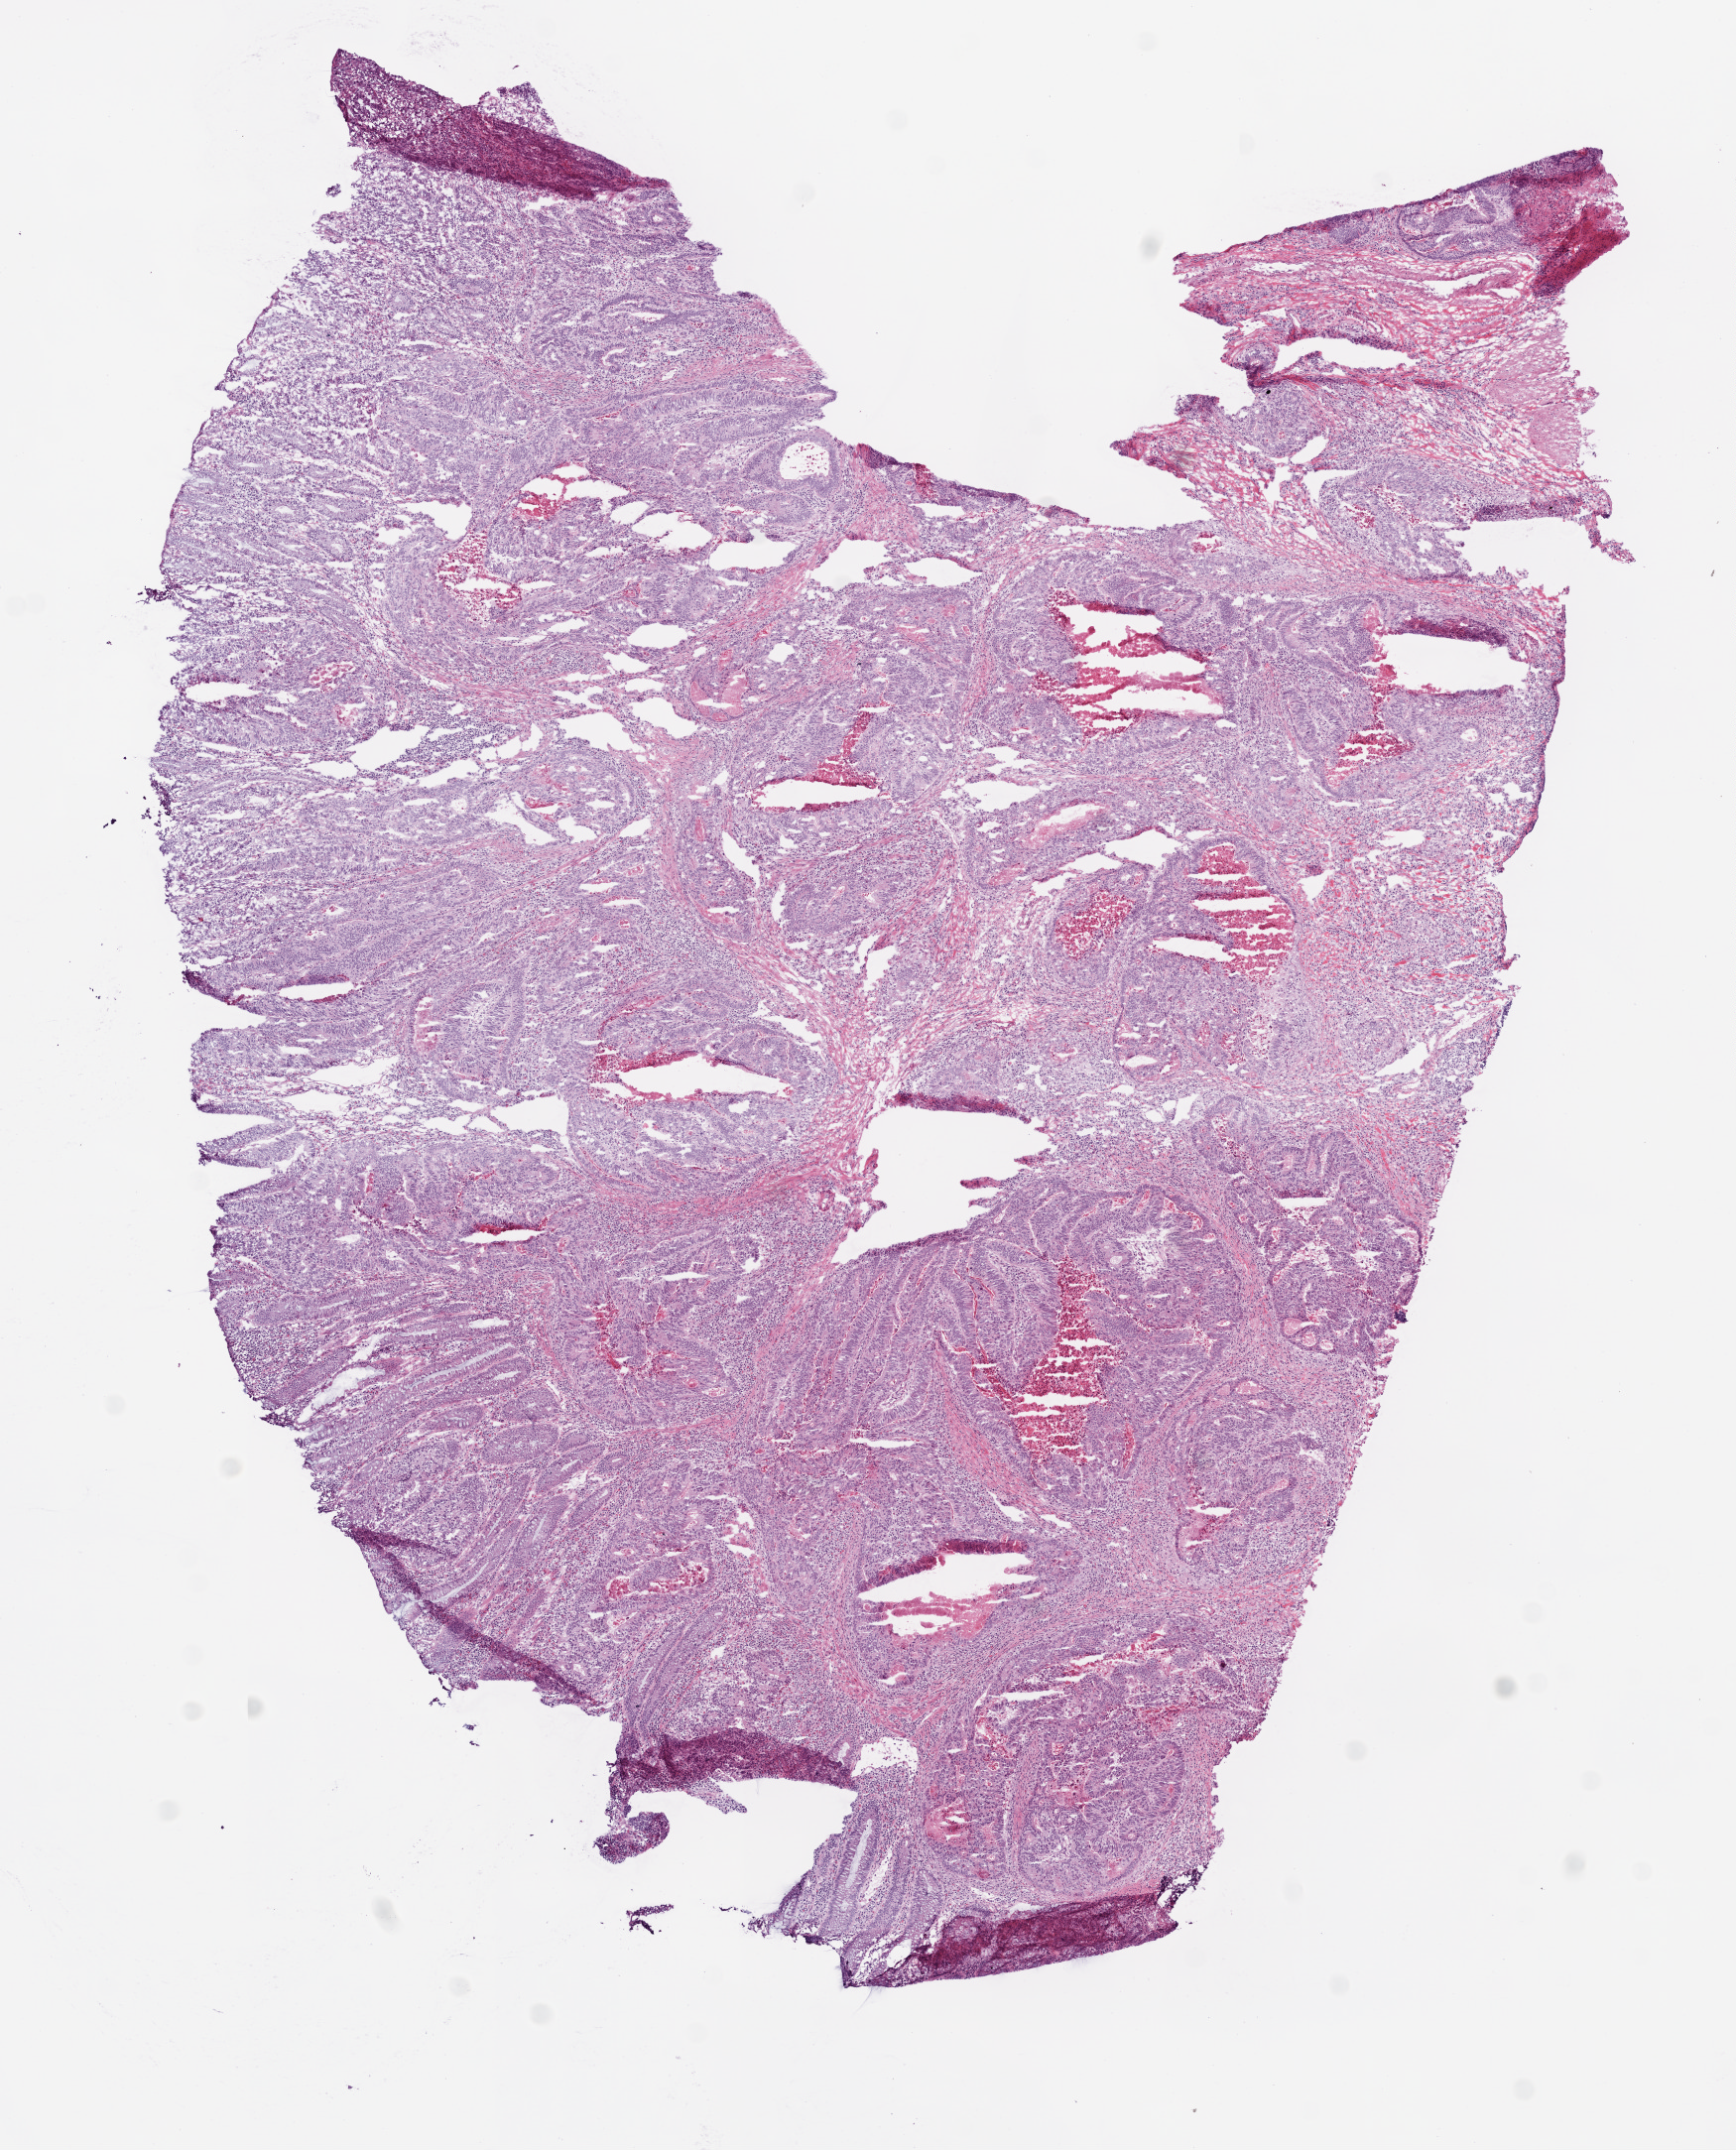
Whole-slide histology image, H&E-stained — a low-resolution overview of the entire scanned area, about 7.0 x 8.7 mm (acquisition: 20x scan), frozen section from the bottom of the tissue portion, colon, primary tumour sample. Male, age 59 years at initial diagnosis. Pathologist review of this section (percent, as recorded): tumour cells 73%, tumour nuclei 80%, normal cells 2%, stromal cells 10%, necrosis 15%.
• lymph nodes positive (case pathology): 0 of 13 examined
• diagnosis: Adenocarcinoma, NOS
• AJCC pathologic stage: IIA (6th edition)